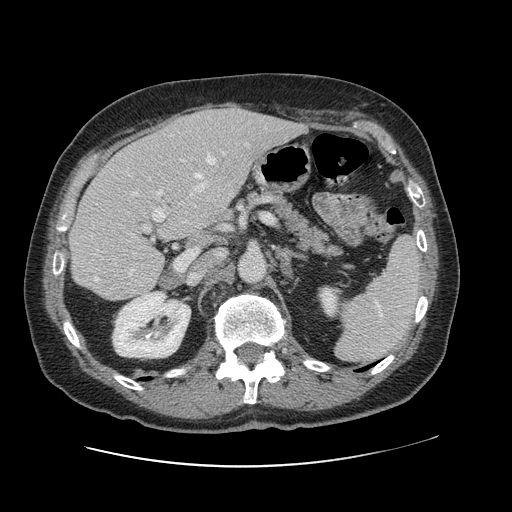
Contrast-enhanced abdominal CT, one axial slice. 120 kVp. Intravenous contrast given. Soft-tissue window (W 400 / L 40 HU). 2.5 mm slice thickness. 512 × 512 image matrix, field of view 402 × 402 mm. Male patient, age 71 years. Case-level facts recorded for this patient, not image findings: diagnosis: colorectal cancer liver metastases, imaged before liver resection; multiple liver metastases: no; largest metastasis: 3.3 cm; disease in both lobes: no.
Annotated regions visible in this slice (manually delineated by an expert):
- hepatic veins: bounding box [x1, y1, x2, y2] px = [91, 156, 227, 281]
- liver: [71, 107, 301, 300]
- planned liver remnant (the part of the liver to remain after resection): [71, 144, 207, 300]
- portal vein (with intrahepatic branches): [97, 143, 249, 251]